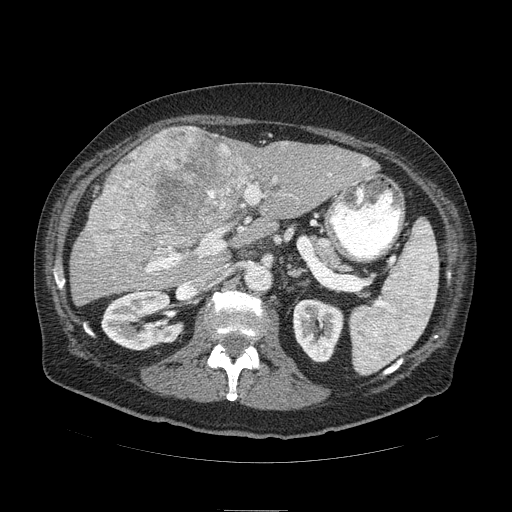
Contrast-enhanced abdominal CT (liver protocol), one axial slice. Reconstruction kernel STANDARD. Soft-tissue window (W 400 / L 40 HU). 2.5 mm slice thickness. 512 × 512 image matrix. From the clinical record (not read from this slice): diagnosis: hepatocellular carcinoma (patient treated with transarterial chemoembolisation; whether this scan precedes or follows treatment is not stated here); TNM stage (as recorded): Stage-IIIA; Child-Pugh class: B; tumour differentiation: well differentiated; tumour size: 13 cm.
Outlined on this slice (semi-automatically segmented with operator editing):
- liver parenchyma outside the tumour (the mass and vessels are separate outlines, so this box may not span the whole liver): box from (x=70, y=126) to (x=378, y=305) px
- mass: (x=87, y=128)–(x=255, y=267)
- liver vessels: (x=146, y=162)–(x=368, y=273)